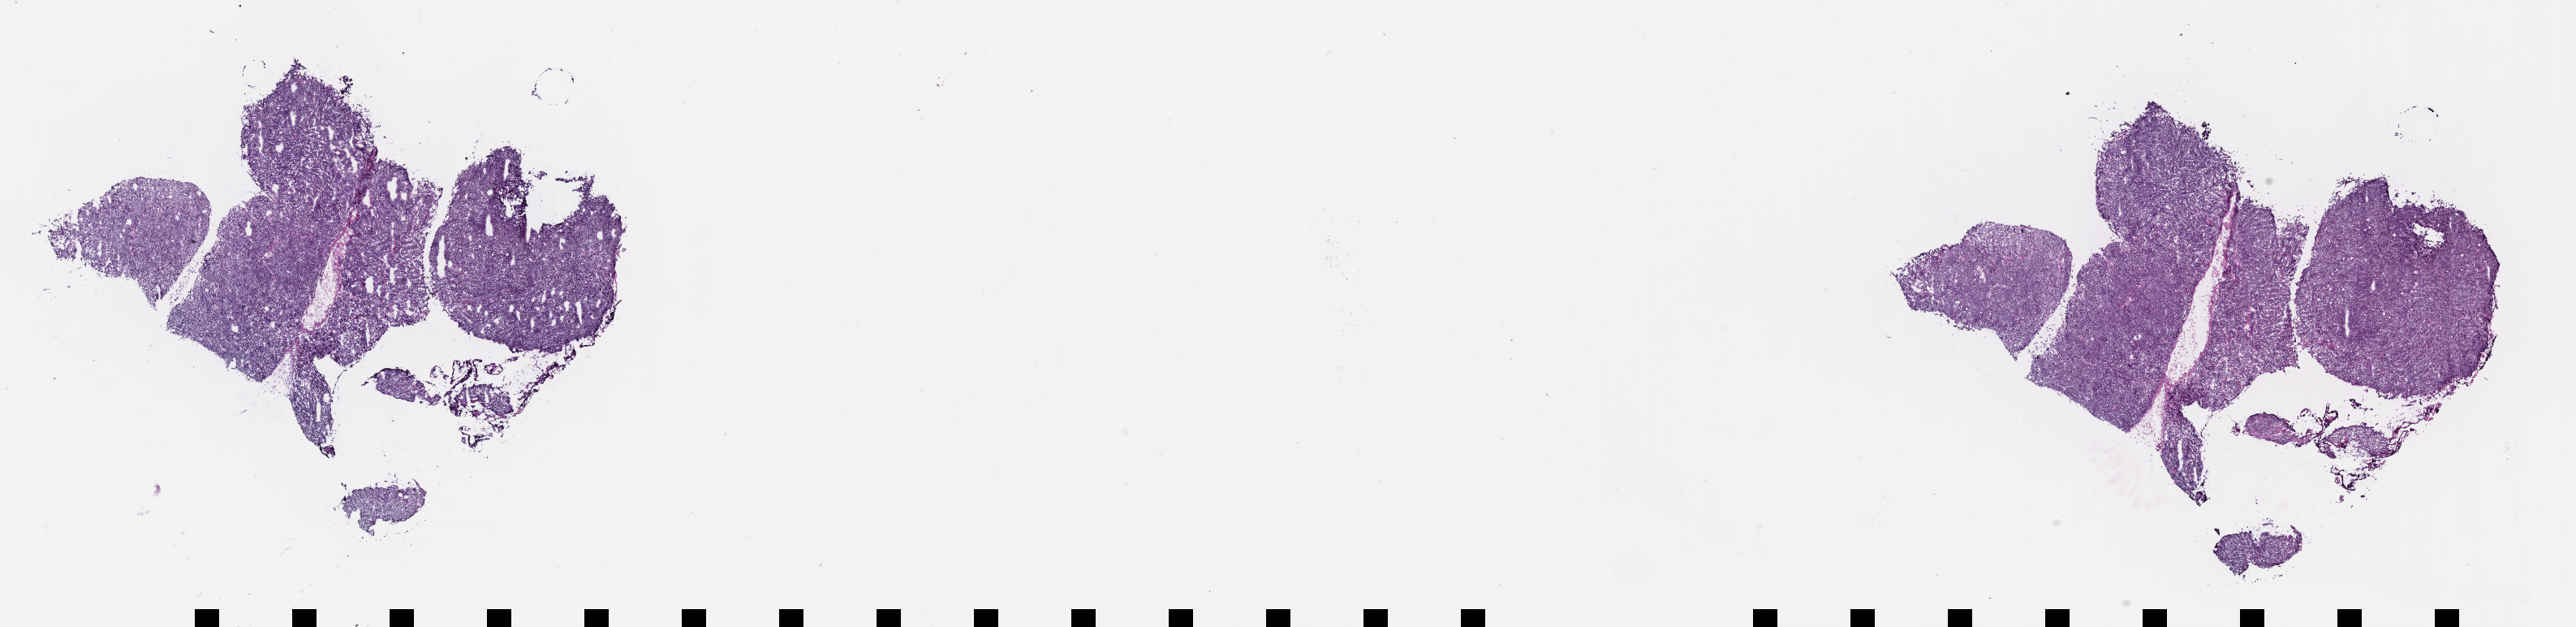
Whole-slide image, hematoxylin and eosin (H&E) stain, whole scanned area (about 25.7 x 6.2 mm) shown as a low-resolution overview, frozen section, specimen: primary tumor, site: peritoneum. Patient: male, age at initial diagnosis 9 years. Composition of this section per pathologist review: tumor cells 90%, tumor nuclei 95%, stromal cells 5%, necrosis 5%, normal cells 0%. Infiltration values recorded for this section: lymphocyte infiltration 3%, monocyte infiltration 3%, neutrophil infiltration 0%.
* Ann Arbor stage (patient): Stage III
* diagnosis: Burkitt lymphoma, NOS